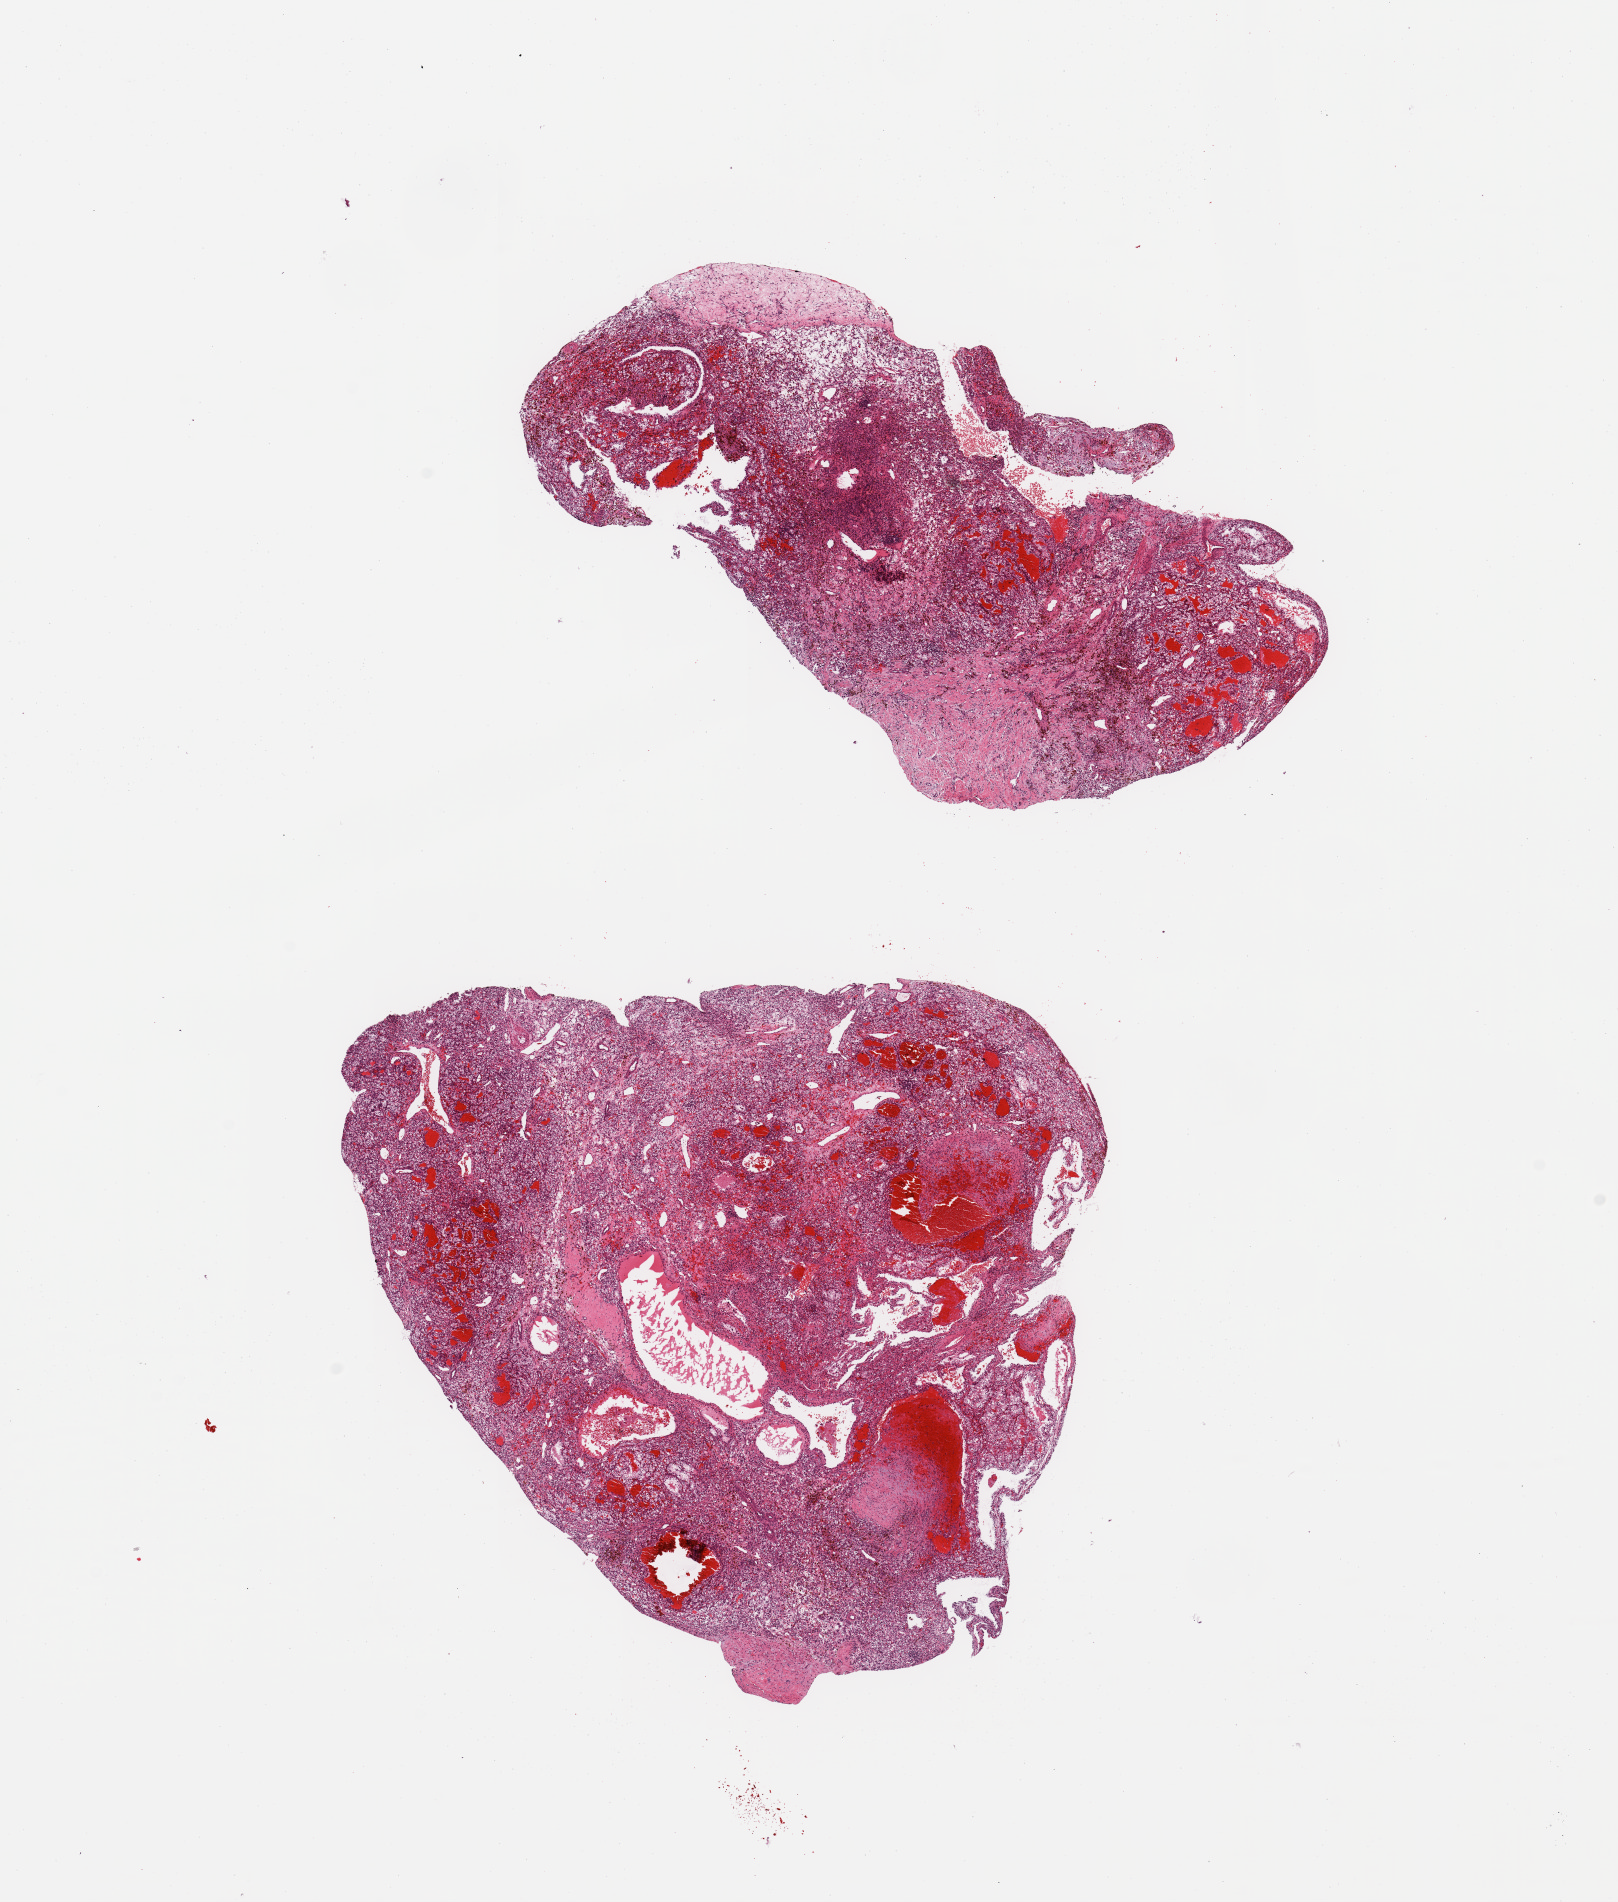
Hematoxylin and eosin (H&E) stained whole-slide image — a low-resolution overview of the entire scanned area, about 12.8 x 15.0 mm (from a 20x scan), tumour tissue sample, sampled site: kidney. 48-year-old male patient. Histologic grade: G2 (moderately differentiated). Slide review estimates, as recorded: tumour nuclei 80%, necrosis 5%.
Primary tumour site (as recorded): middle. AJCC pathologic stage: I. Diagnosis: Renal cell carcinoma, NOS.